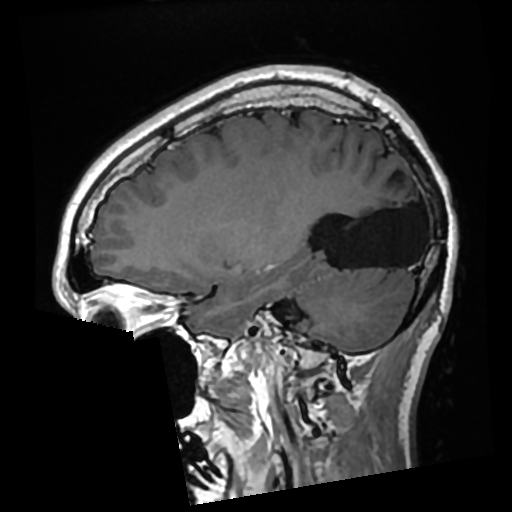
Brain MRI from a brain-tumour surgery series, one sagittal slice. Slice 102 of 276 in the series (ordered by position). T1-weighted post-contrast. 0.7 mm slice thickness. 512 × 512 image matrix, field of view 250 × 250 mm. Case-level facts recorded for this patient, not image findings: histopathology: Glioma with ependymal features; WHO grade: 2; tumour location: Left Parietal.
Annotated regions visible in this slice (manually delineated by an expert):
- previous resection cavity: bounding box <327,182,423,268> (left, top, right, bottom; pixels)